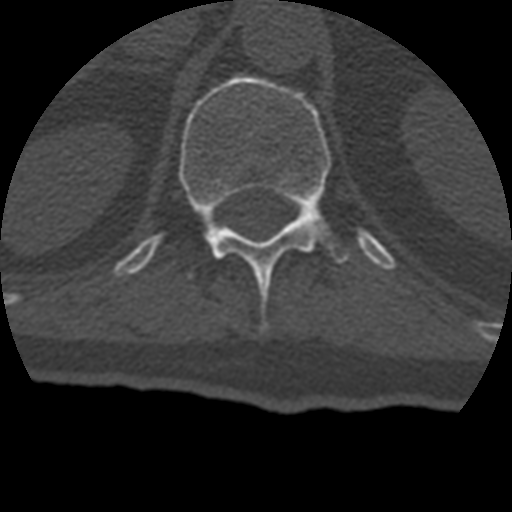
CT including the spine, one axial slice; slice 170 of 399 in the series (ordered by position); bone window (W 1800 / L 400 HU); 1.25 mm slice thickness; 512 × 512 image matrix, field of view 160 × 160 mm. Patient age 69 years. From the clinical record (not read from this slice): primary cancer: prostate.
Structures marked on this image (semi-automatic segmentation, software-assisted and operator-edited):
- T12 vertebra: bounding box (x1, y1, x2, y2) in pixels: (179, 75, 348, 290)